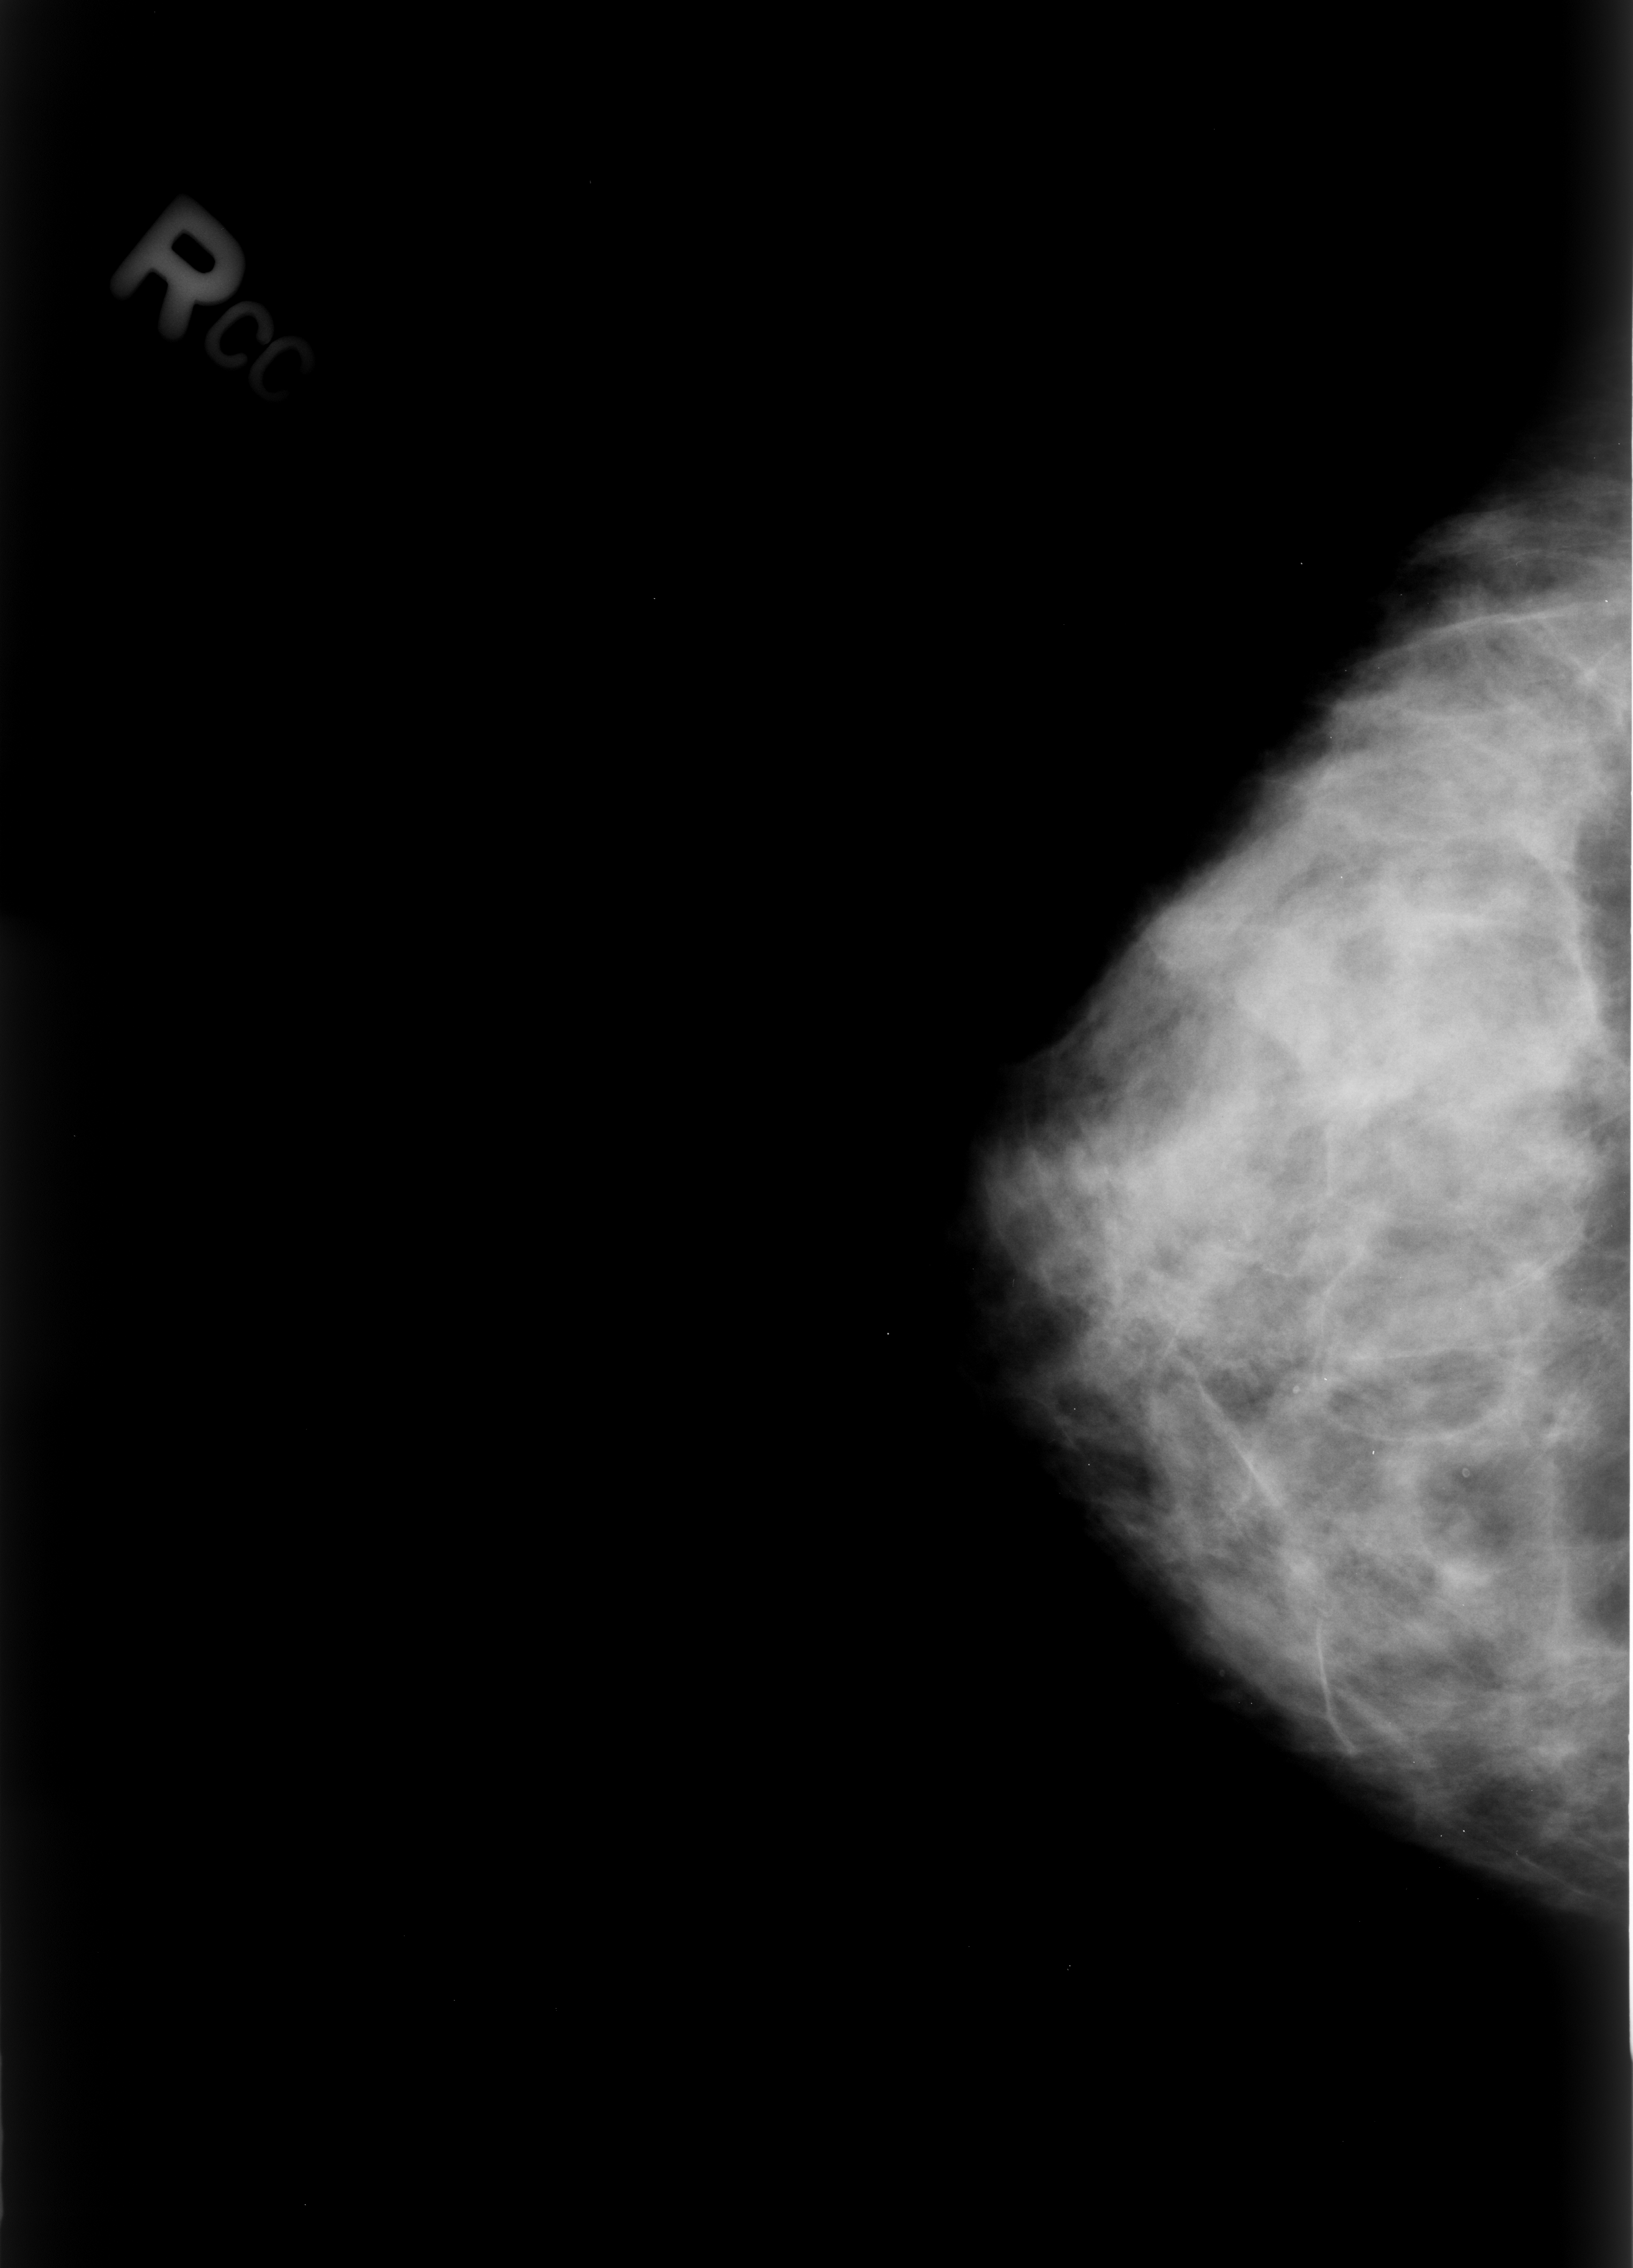
Digitized screen-film mammogram, right breast, craniocaudal (CC) view.
Marked findings (only marked abnormalities are described; nothing is implied about the rest of the image): Finding 1 of 2: calcifications, morphology lucent center; BI-RADS assessment category 2; benign; no additional work-up was recommended (benign without callback). Finding 2 of 2: calcifications, morphology lucent center; BI-RADS assessment category 2; subtlety rating 4 on a 1 (subtle) to 5 (obvious) scale; benign; no additional work-up was recommended (benign without callback).